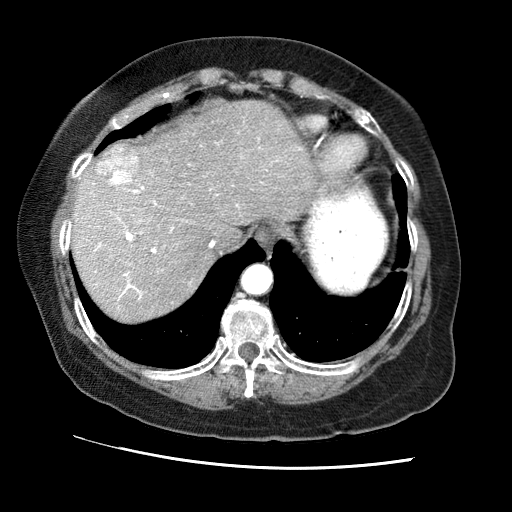
Contrast-enhanced abdominal CT (liver protocol), one axial slice. Position 54 of 65 along the scan axis. Reconstruction kernel STANDARD. Soft-tissue window (W 400 / L 40 HU). 2.5 mm slice thickness. 512 × 512 image matrix. From the clinical record (not read from this slice): diagnosis: hepatocellular carcinoma (patient treated with transarterial chemoembolisation; whether this scan precedes or follows treatment is not stated here); TNM stage (as recorded): Stage-II; Child-Pugh class: A; tumour differentiation: no biopsy; tumour nodularity: multinodular.
Structures marked on this image (semi-automatically segmented with operator editing):
- abdominal aorta: box from (x=243, y=266) to (x=272, y=294) px
- liver parenchyma outside the tumour (the mass and vessels are separate outlines, so this box may not span the whole liver): (x=70, y=100)–(x=318, y=320)
- mass: (x=96, y=140)–(x=141, y=186)
- liver vessels: (x=76, y=186)–(x=238, y=300)